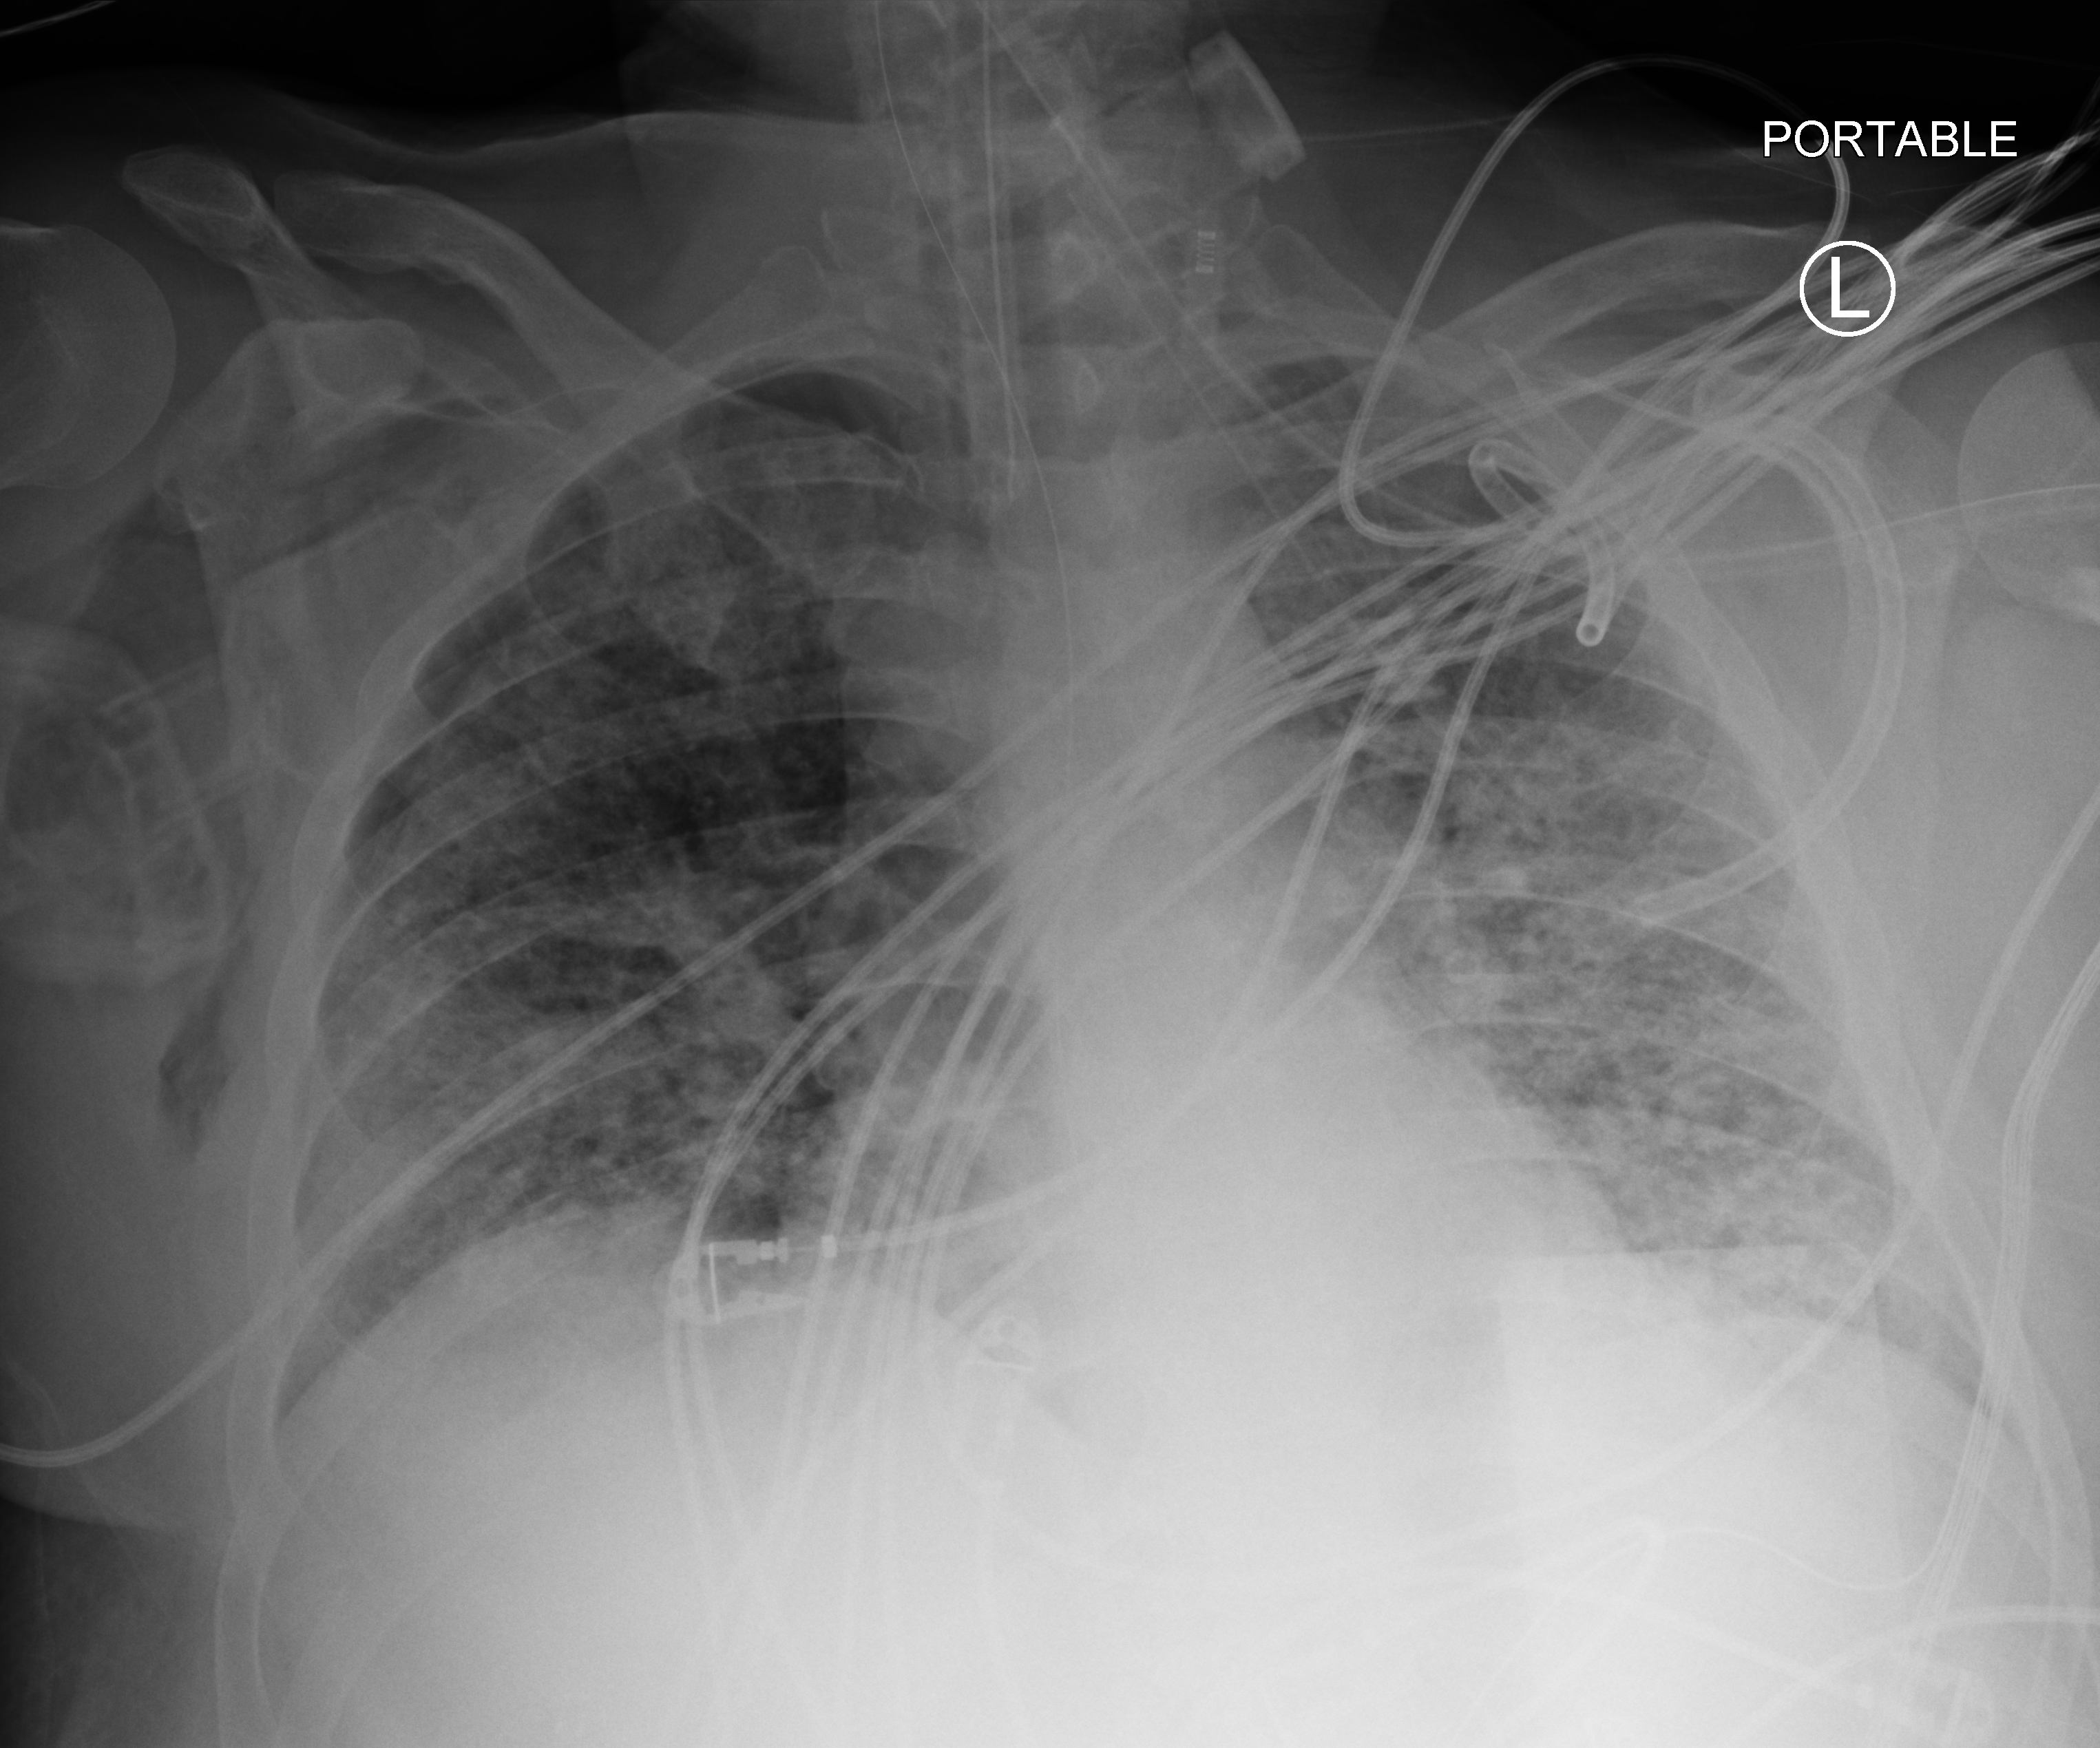
Portable chest radiograph, anteroposterior (AP) projection. Adult patient hospitalised with COVID-19, age 18–59 years.
Hospital-stay facts (about this admission, not read from this image; timing relative to this image not recorded):
- mechanically ventilated during this hospital stay: yes